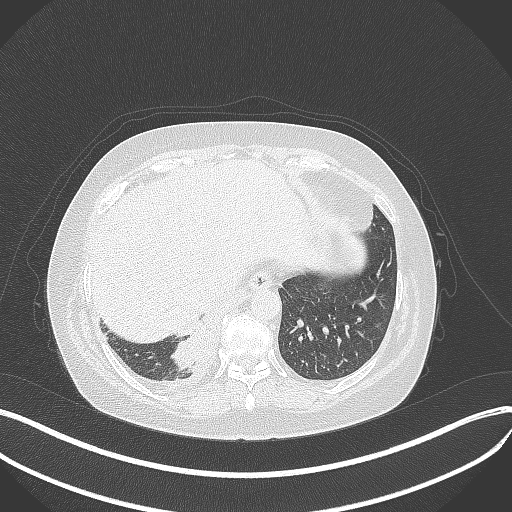
Chest CT, one axial slice; position 85 of 381 along the scan axis; reconstruction kernel B70f; lung window (W 1500 / L -600 HU); 512 × 512 image matrix. Patient: female, 56 years. Case-level facts recorded for this patient, not image findings: clinical TNM (as recorded): T2b N1 M0; histopathological grade: G3.
Outlined on this slice (rectangle marked by the reading radiologist):
- lung tumour (recorded histology: small cell carcinoma): bounding box <169,327,218,372> (left, top, right, bottom; pixels)